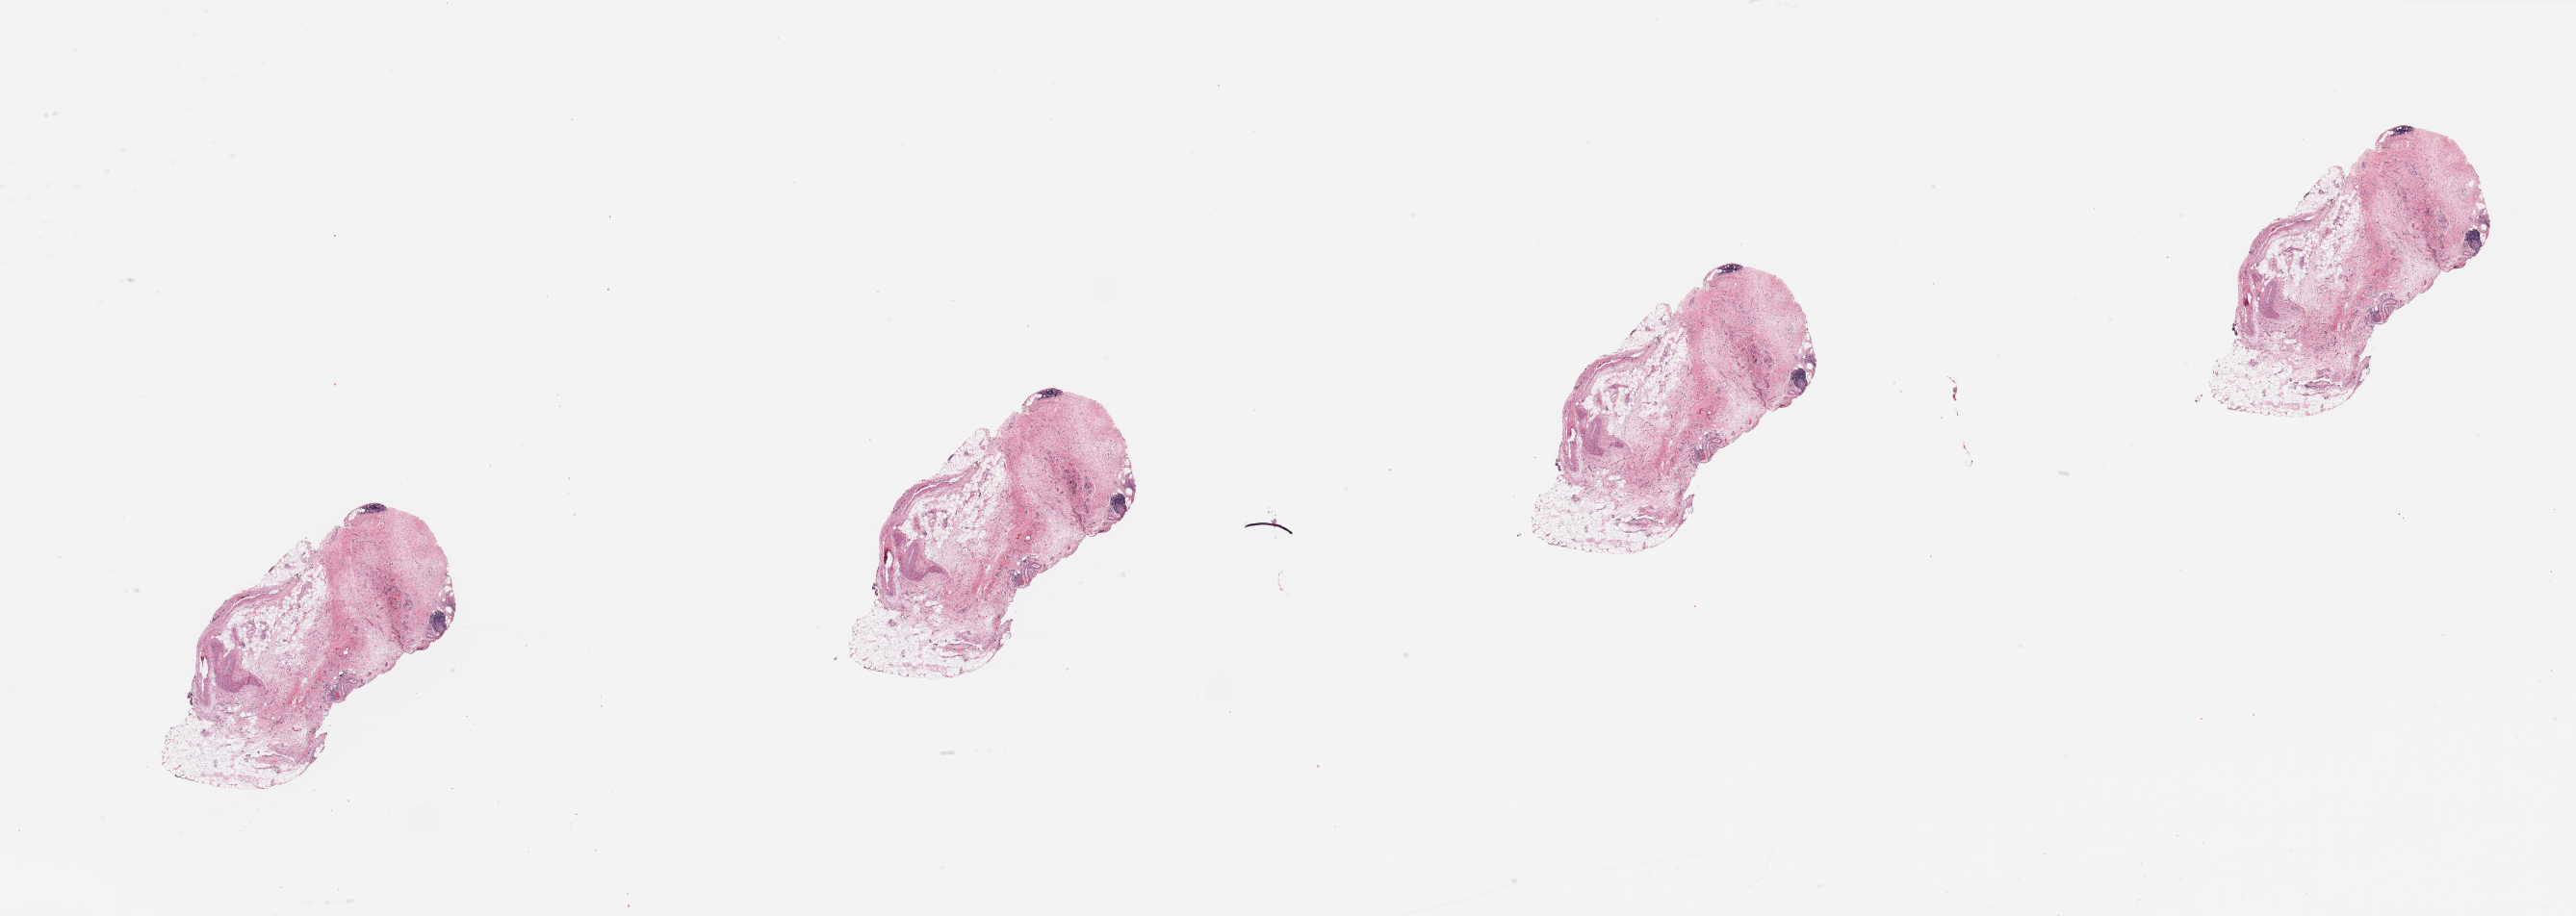
H&E whole-slide image, whole scanned area (about 42.3 x 15.1 mm, from a 20x scan) shown as a low-resolution overview. Pancreas, tumour tissue. 74-year-old female patient.
Primary tumour site (as recorded): head. Patient diagnosis (cohort enrolment): ductal adenocarcinoma (pancreas).